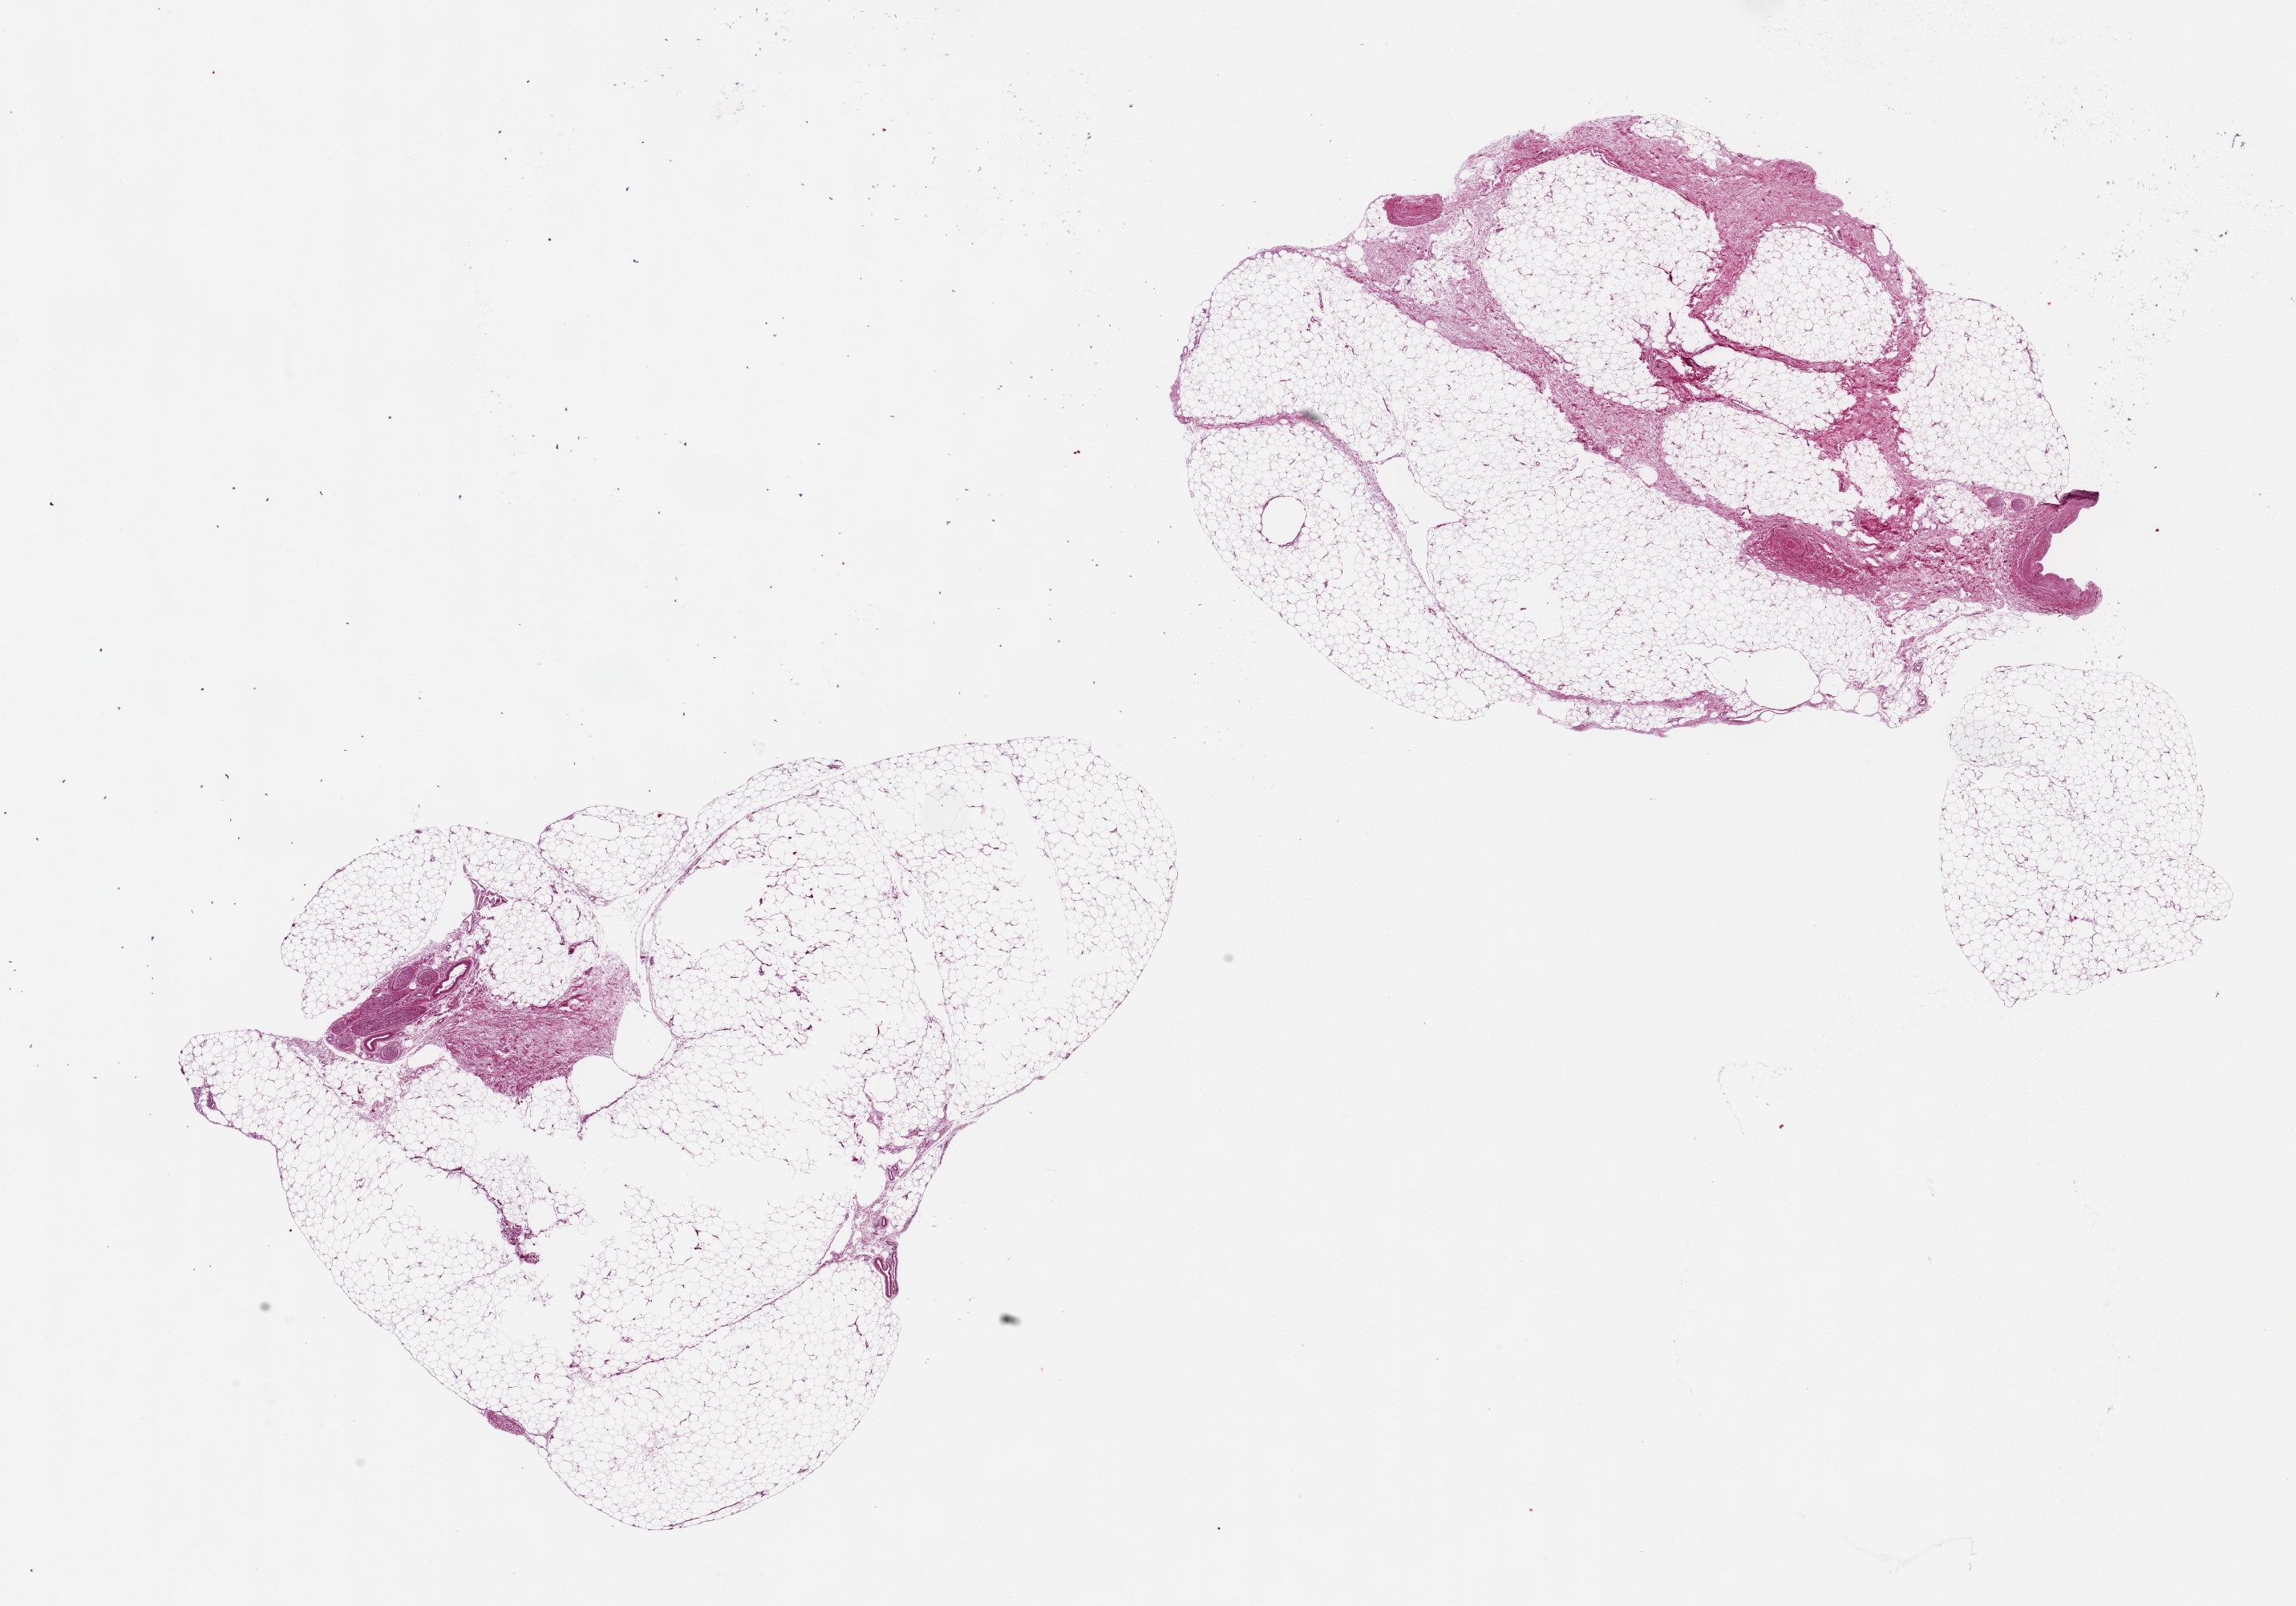
Haematoxylin and eosin whole-slide image — low-resolution overview of the scanned area, about 22.6 x 15.8 mm, PAXgene-fixed, paraffin-embedded tissue, section of adipose tissue (target tissue), donor tissue sample. Donor: female.
Reviewer comment on this tissue sample: 2 pieces, 9x7 & 11x 6mm.